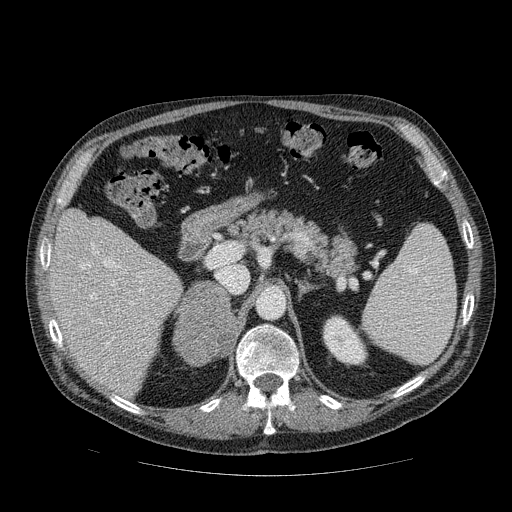
Contrast-enhanced abdominal CT, one axial slice. Slice 56 of 111 in the series (ordered by position). Reconstruction kernel STANDARD. Intravenous contrast given. Soft-tissue window (W 400 / L 40 HU). 2.5 mm slice thickness. 512 × 512 image matrix, field of view 420 × 420 mm. Male patient, age 56 years. Case-level facts recorded for this patient, not image findings: diagnosis: adrenocortical carcinoma; tumour side: right adrenal; tumour size at pathology: 9 cm; Ki-67 index: 48 %; stage (as recorded): 4.
Outlined on this slice (semi-automatic segmentation, software-assisted and operator-edited):
- mass: bounding box <175,284,236,363> (left, top, right, bottom; pixels)